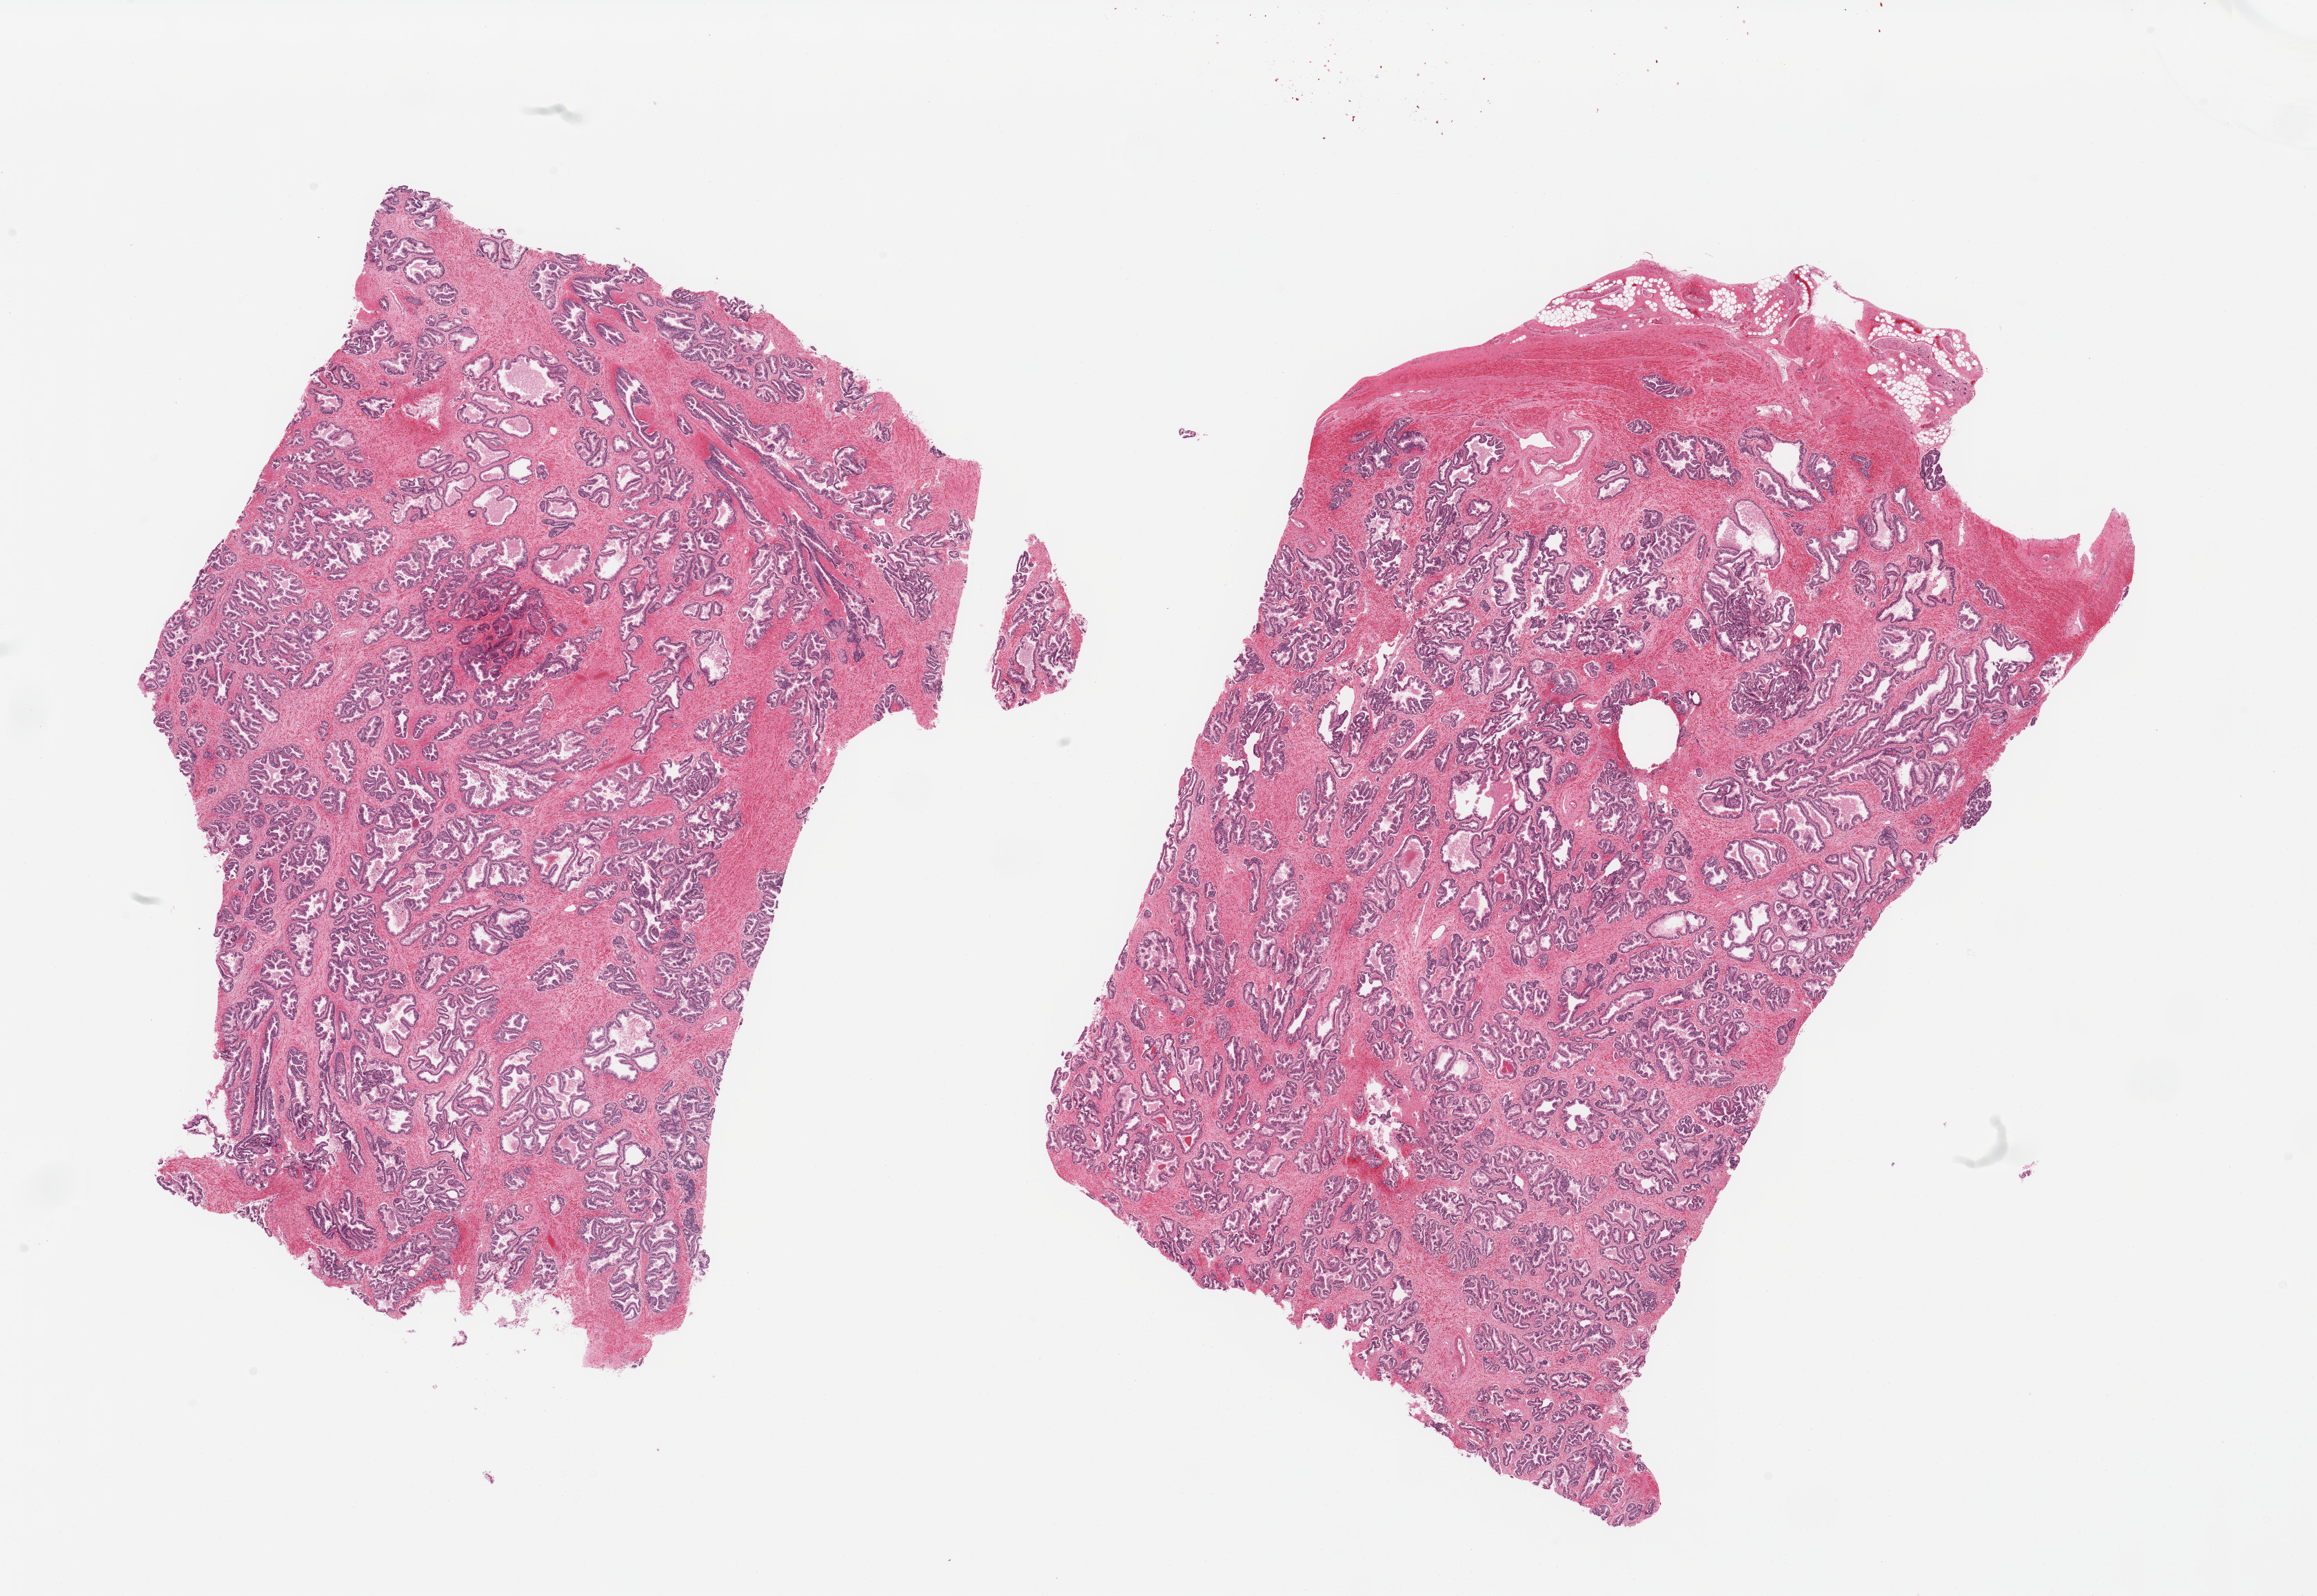
Digitized hematoxylin and eosin (H&E)-stained section — shown as a low-resolution overview of the whole scanned area (about 26.6 x 18.3 mm). PAXgene-fixed, paraffin-embedded tissue. Section of prostate (target tissue). Donor tissue sample.
- reviewer comment on this tissue sample: 2 pieces; unusually well preserved glands; 3x0.5mm fibrofatty cap at 1 end of 1 piece